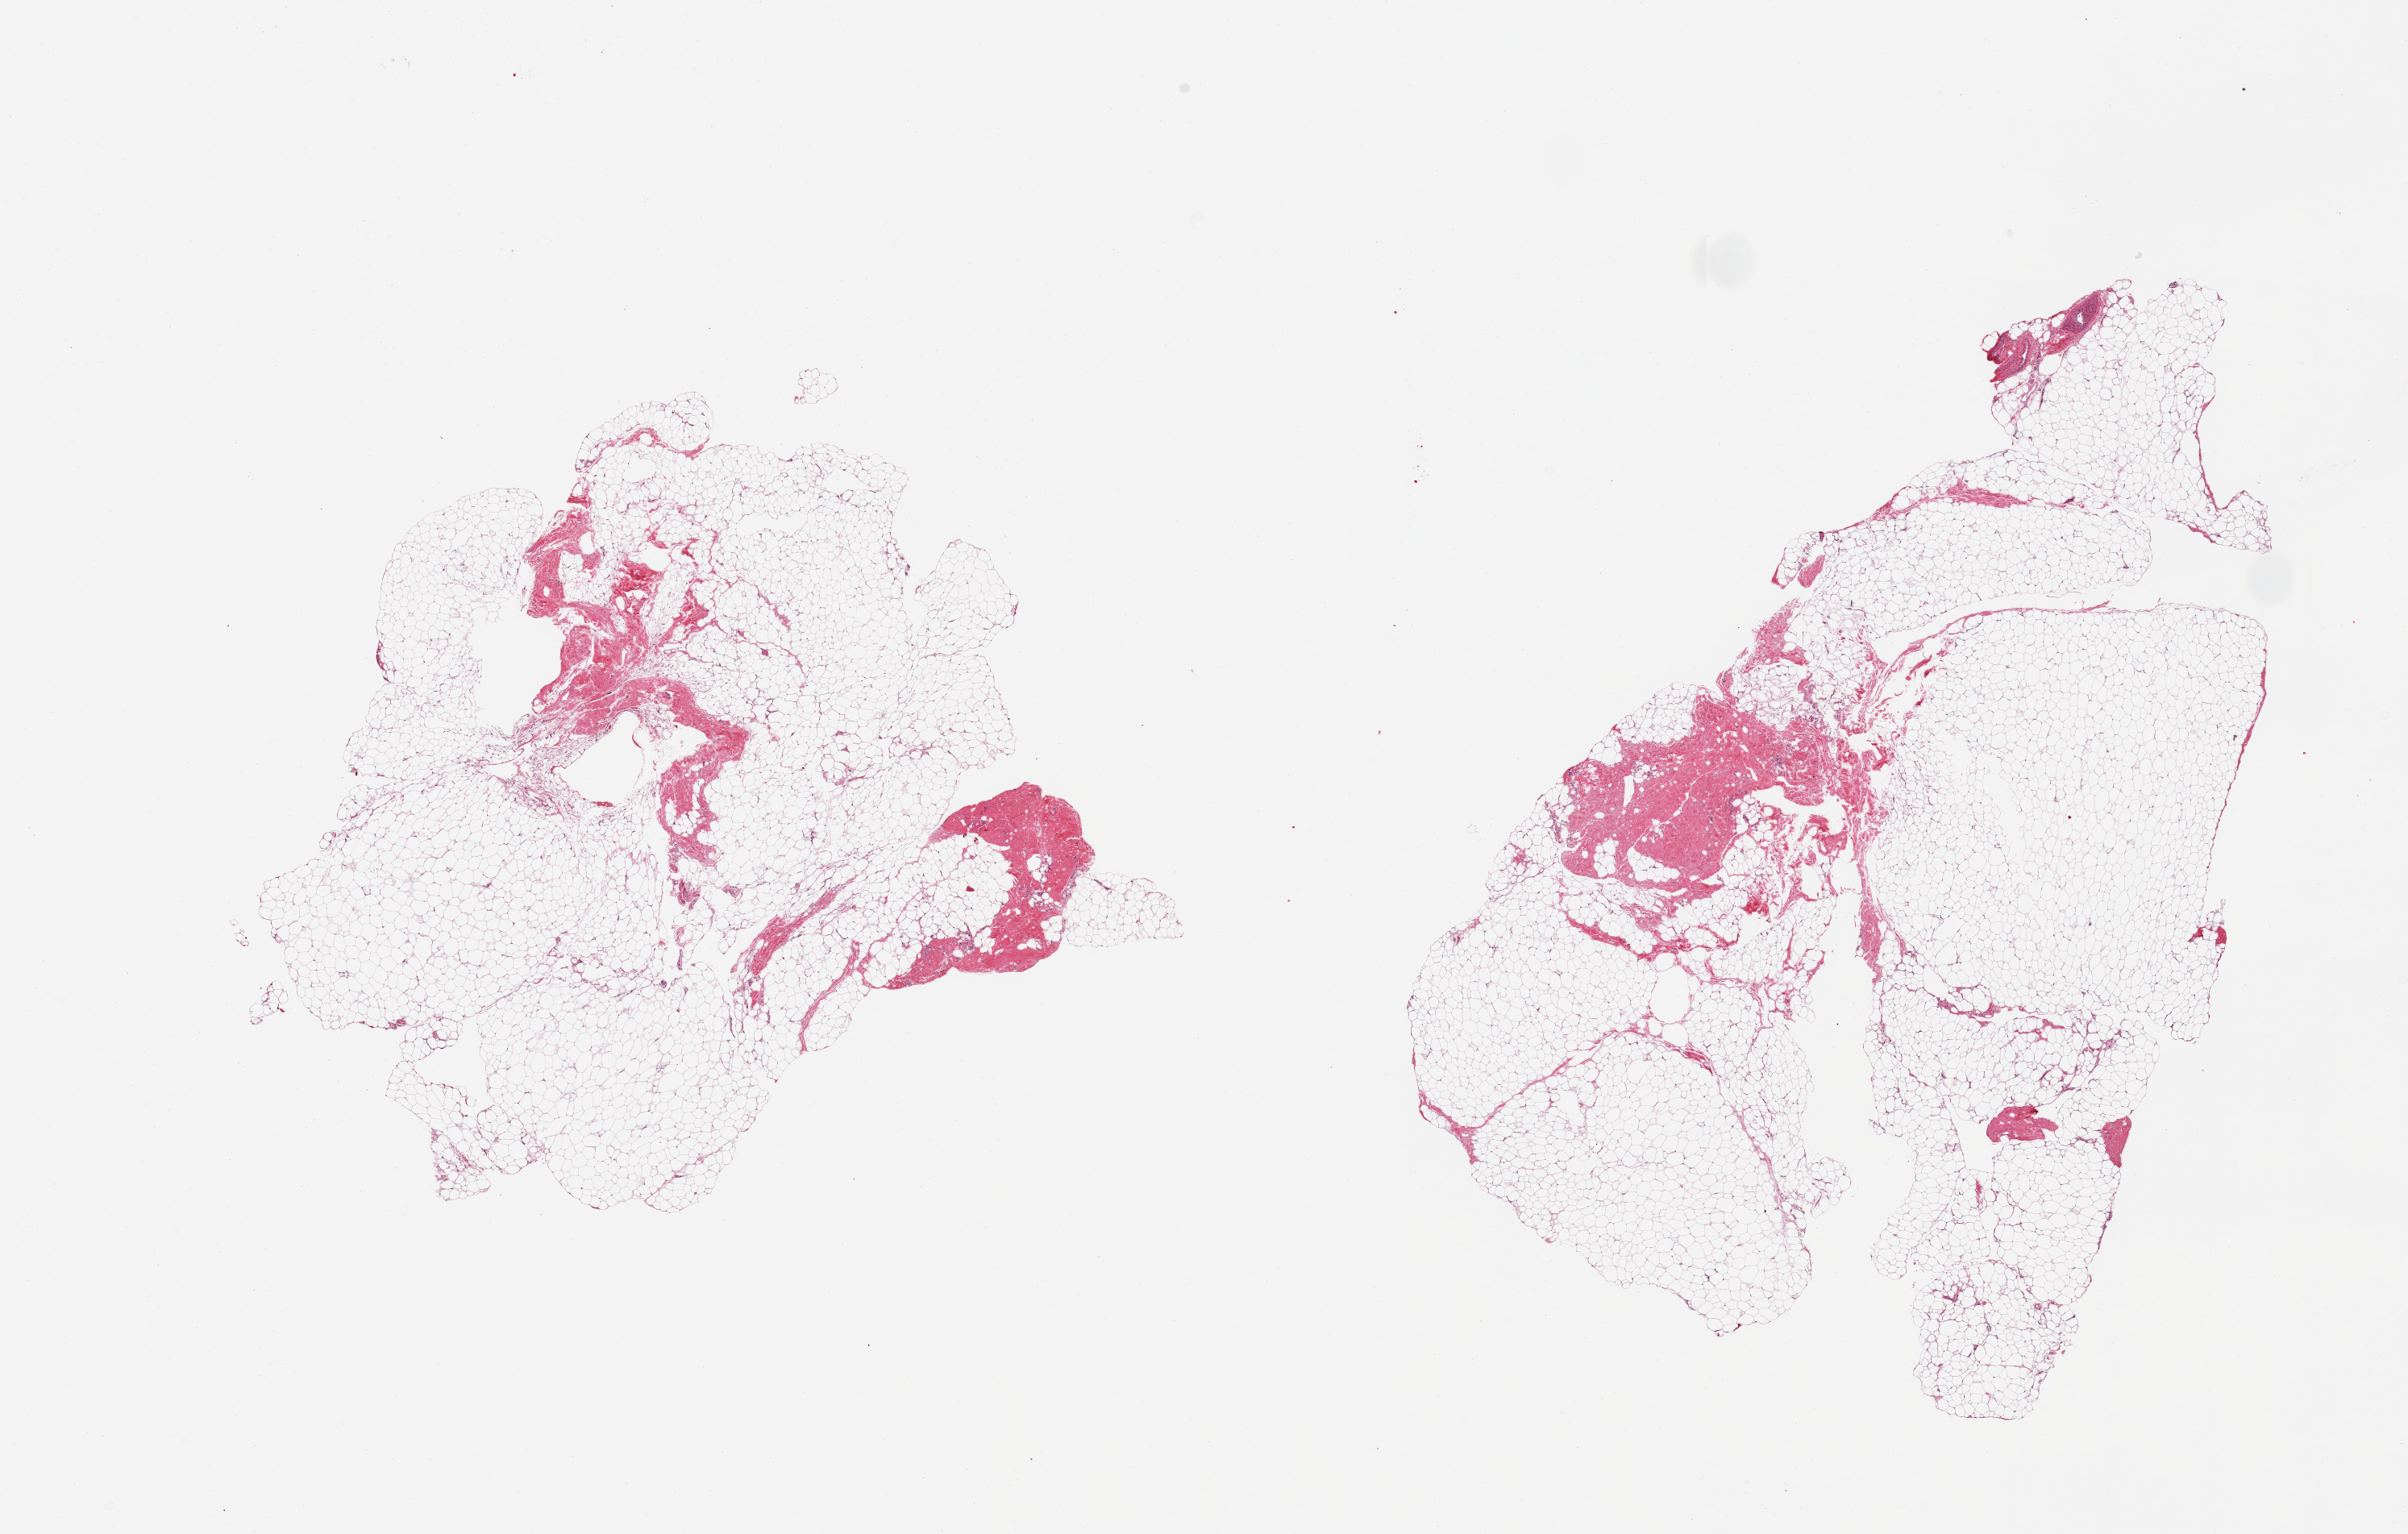
Digitized haematoxylin and eosin-stained section, brightfield, whole scanned area (about 23.6 x 15.1 mm) shown as a low-resolution overview, PAXgene-fixed, paraffin-embedded tissue, sampled site (target tissue): breast, donor tissue sample. Donor: male.
Reviewer comment on this tissue sample: 2 pieces; adipose tissue and ~10 to 20% fibrovasular component.